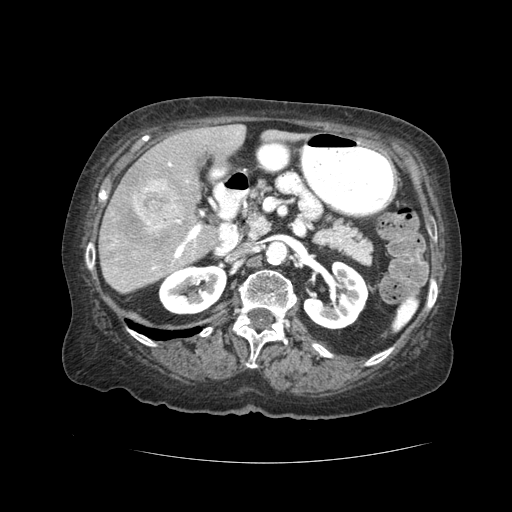
Contrast-enhanced abdominal CT (liver protocol), one axial slice; position 14 of 59 along the scan axis; reconstruction kernel STANDARD; soft-tissue window (W 400 / L 40 HU); 512 × 512 image matrix, field of view 380 × 380 mm. From the clinical record (not read from this slice): diagnosis: hepatocellular carcinoma (patient treated with transarterial chemoembolisation; whether this scan precedes or follows treatment is not stated here); TNM stage (as recorded): Stage-I; Child-Pugh class: A; tumour nodularity: uninodular.
Annotated regions visible in this slice (semi-automatically segmented with operator editing):
- liver parenchyma outside the tumour (the mass and vessels are separate outlines, so this box may not span the whole liver): box from (x=98, y=124) to (x=246, y=293) px
- mass: (x=132, y=179)–(x=181, y=233)
- liver vessels: (x=145, y=132)–(x=239, y=270)